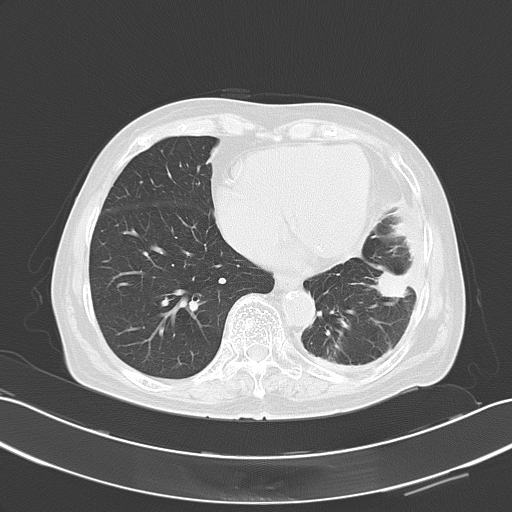
Chest CT, one axial slice. Position 21 of 60 along the scan axis. 120 kVp. Lung window (W 1500 / L -600 HU). 5 mm slice thickness. 512 × 512 image matrix, field of view 353 × 353 mm. Patient: female, 82 years. From the clinical record (not read from this slice): clinical TNM (as recorded): T1c N0 M1.
Annotated regions visible in this slice (bounding box drawn by a radiologist):
- lung tumour (recorded histology: adenocarcinoma): bounding box (x1, y1, x2, y2) in pixels: (373, 263, 413, 303)